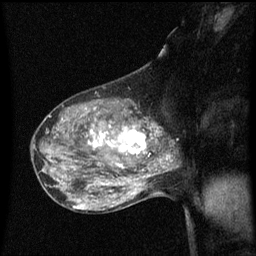
Breast MRI (dynamic contrast-enhanced), one sagittal slice. Position 36 of 60 along the scan axis. Dynamic contrast-enhanced series, image 2 of 3 at this slice position (ordered by acquisition). 1.5 T. TE 4.2 ms, TR 8.4 ms. 2 mm slice thickness. 256 × 256 image matrix, field of view 200 × 200 mm. Patient: female, 50 years.
Annotated regions visible in this slice (semi-automatically segmented with operator editing):
- analysis volume of interest (the breast-tissue region the enhancement analysis was run in; not a lesion): bounding box [x1, y1, x2, y2] px = [100, 114, 153, 171]
- tumour enhancement mask (voxels above the 70 % enhancement threshold inside the analysis volume of interest): [100, 126, 153, 171]